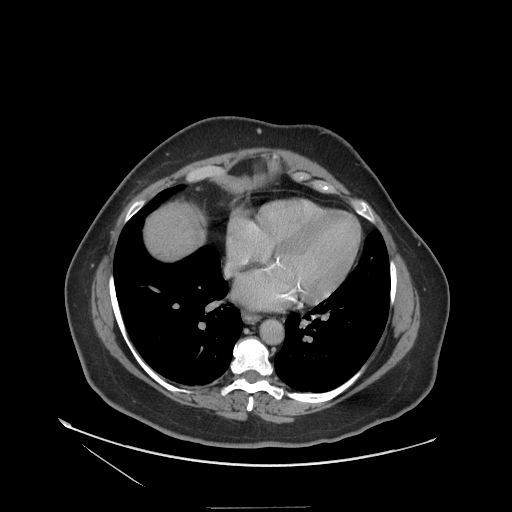
Contrast-enhanced abdominal CT (liver protocol), one axial slice; position 111 of 127 along the scan axis; reconstruction kernel STANDARD; soft-tissue window (W 400 / L 40 HU); 2.5 mm slice thickness; 512 × 512 image matrix. From the clinical record (not read from this slice): diagnosis: hepatocellular carcinoma (patient treated with transarterial chemoembolisation; whether this scan precedes or follows treatment is not stated here); TNM stage (as recorded): Stage-II; Child-Pugh class: A; tumour differentiation: well differentiated; tumour nodularity: multinodular.
Annotated regions visible in this slice (semi-automatically segmented with operator editing):
- liver parenchyma outside the tumour (the mass and vessels are separate outlines, so this box may not span the whole liver): bounding box <144,204,202,260> (left, top, right, bottom; pixels)